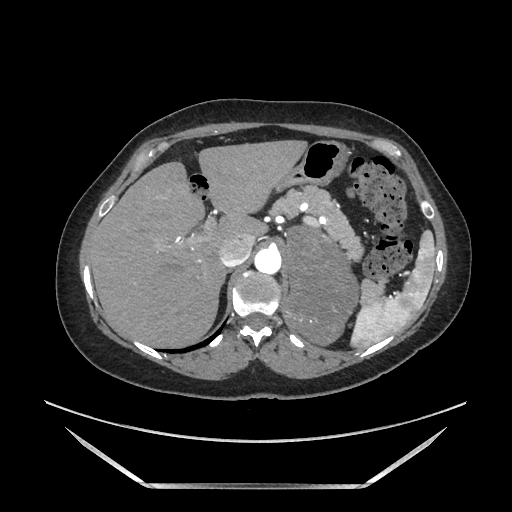
Contrast-enhanced abdominal CT, one axial slice; slice 129 of 205 in the series (ordered by position); soft-tissue window (W 400 / L 40 HU); 512 × 512 image matrix, field of view 440 × 440 mm. Female patient. From the clinical record (not read from this slice): diagnosis: adrenocortical carcinoma; tumour side: left adrenal.
Structures marked on this image (semi-automatically segmented with operator editing):
- mass: bounding box (x1, y1, x2, y2) in pixels: (288, 228, 357, 343)